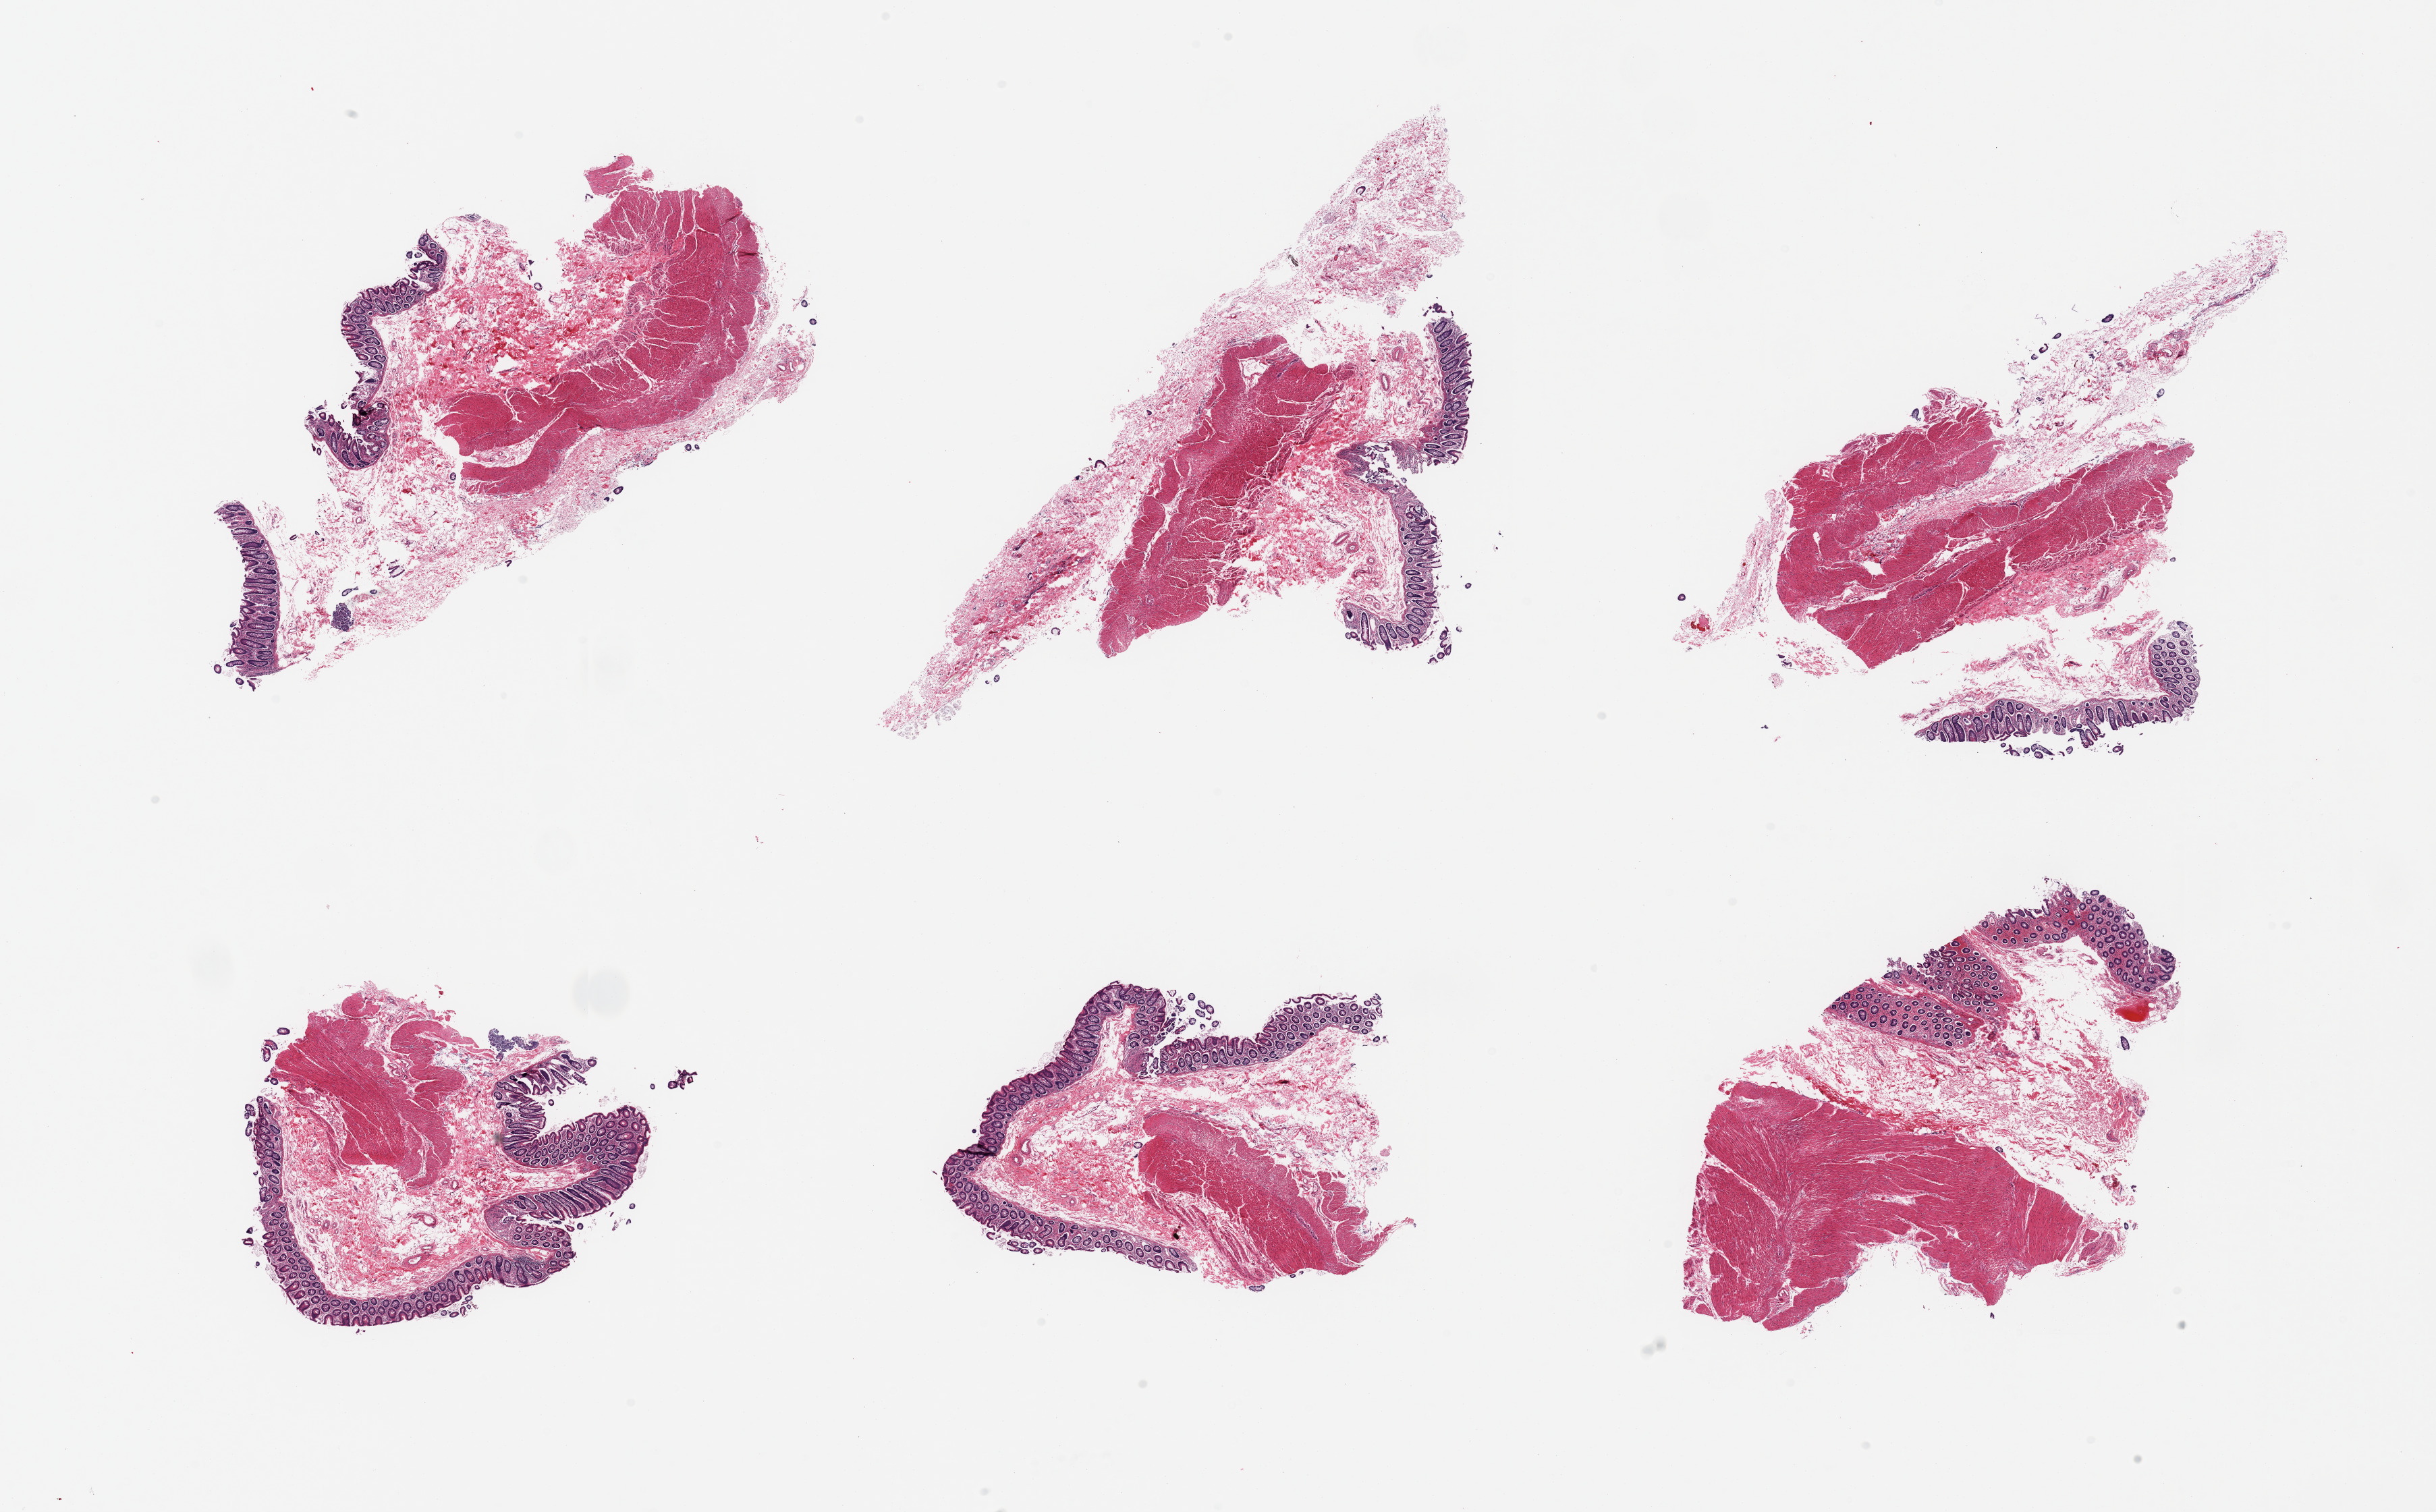
Digitized H&E-stained section — a low-resolution overview of the entire scanned area, about 28.5 x 17.7 mm. PAXgene-fixed paraffin-embedded (PFPE) section. Target tissue: ileum. Tissue donor sample.
Reviewer comment on this tissue sample: 6 pieces; full thickness colon, not ileum.